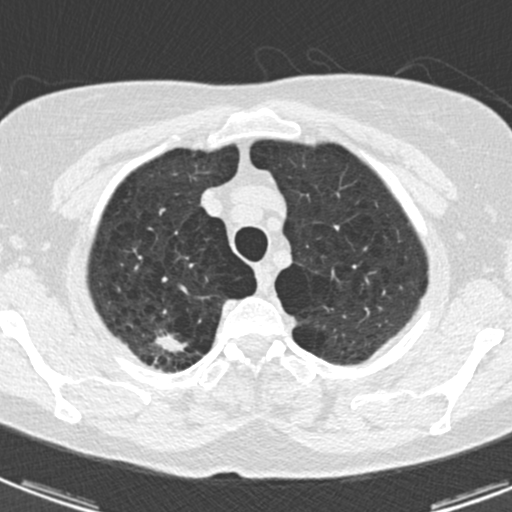
Low-dose screening chest CT, one axial slice; position 151 of 174 along the scan axis; reconstruction kernel B30f; lung window (W 1500 / L -600 HU); 512 × 512 image matrix.
Structures marked on this image (expert manual segmentation):
- lesion 1 (tumor, upper lobe of right lung): bounding box <156,333,188,352> (left, top, right, bottom; pixels)